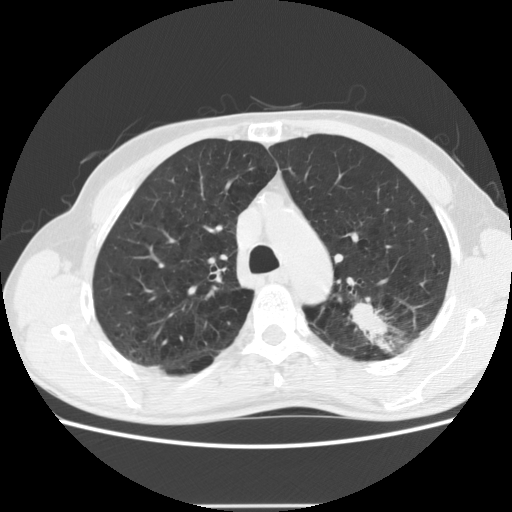
Low-dose screening chest CT, one axial slice; slice 142 of 191 in the series (ordered by position); lung window (W 1500 / L -600 HU); 2.5 mm slice thickness; 512 × 512 image matrix, field of view 352 × 352 mm.
Outlined on this slice (manually delineated by an expert):
- lesion 1 (tumor, upper lobe of left lung): box from (x=351, y=302) to (x=388, y=344) px